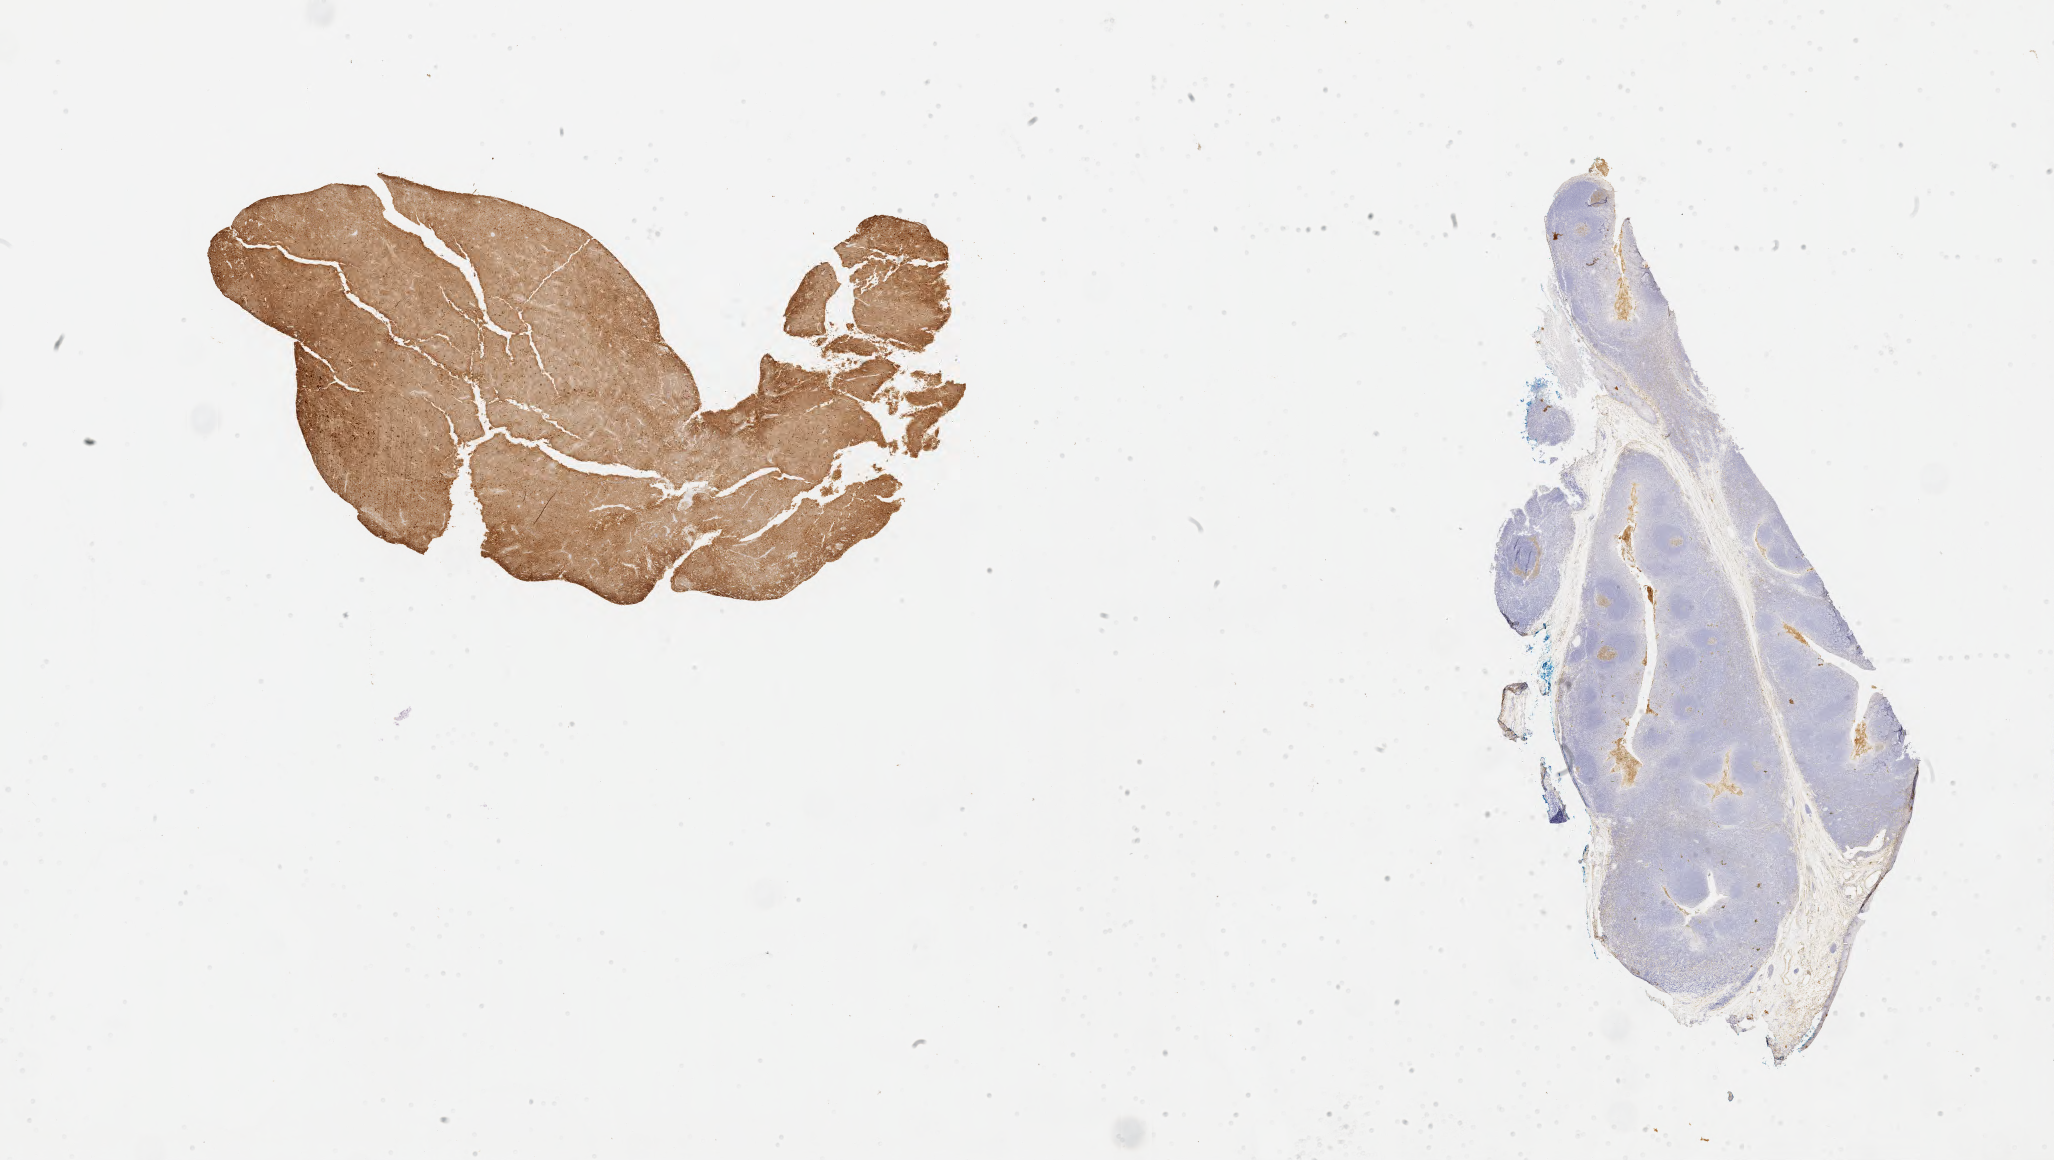
Whole-slide image, immunohistochemical stain for CD10 — whole scanned area (about 33.2 x 18.7 mm) shown as a low-resolution overview. Specimen: tumor tissue. Site: lymph node of head and neck. Patient: male, age at initial diagnosis 5 years.
• diagnosis: Burkitt lymphoma, NOS